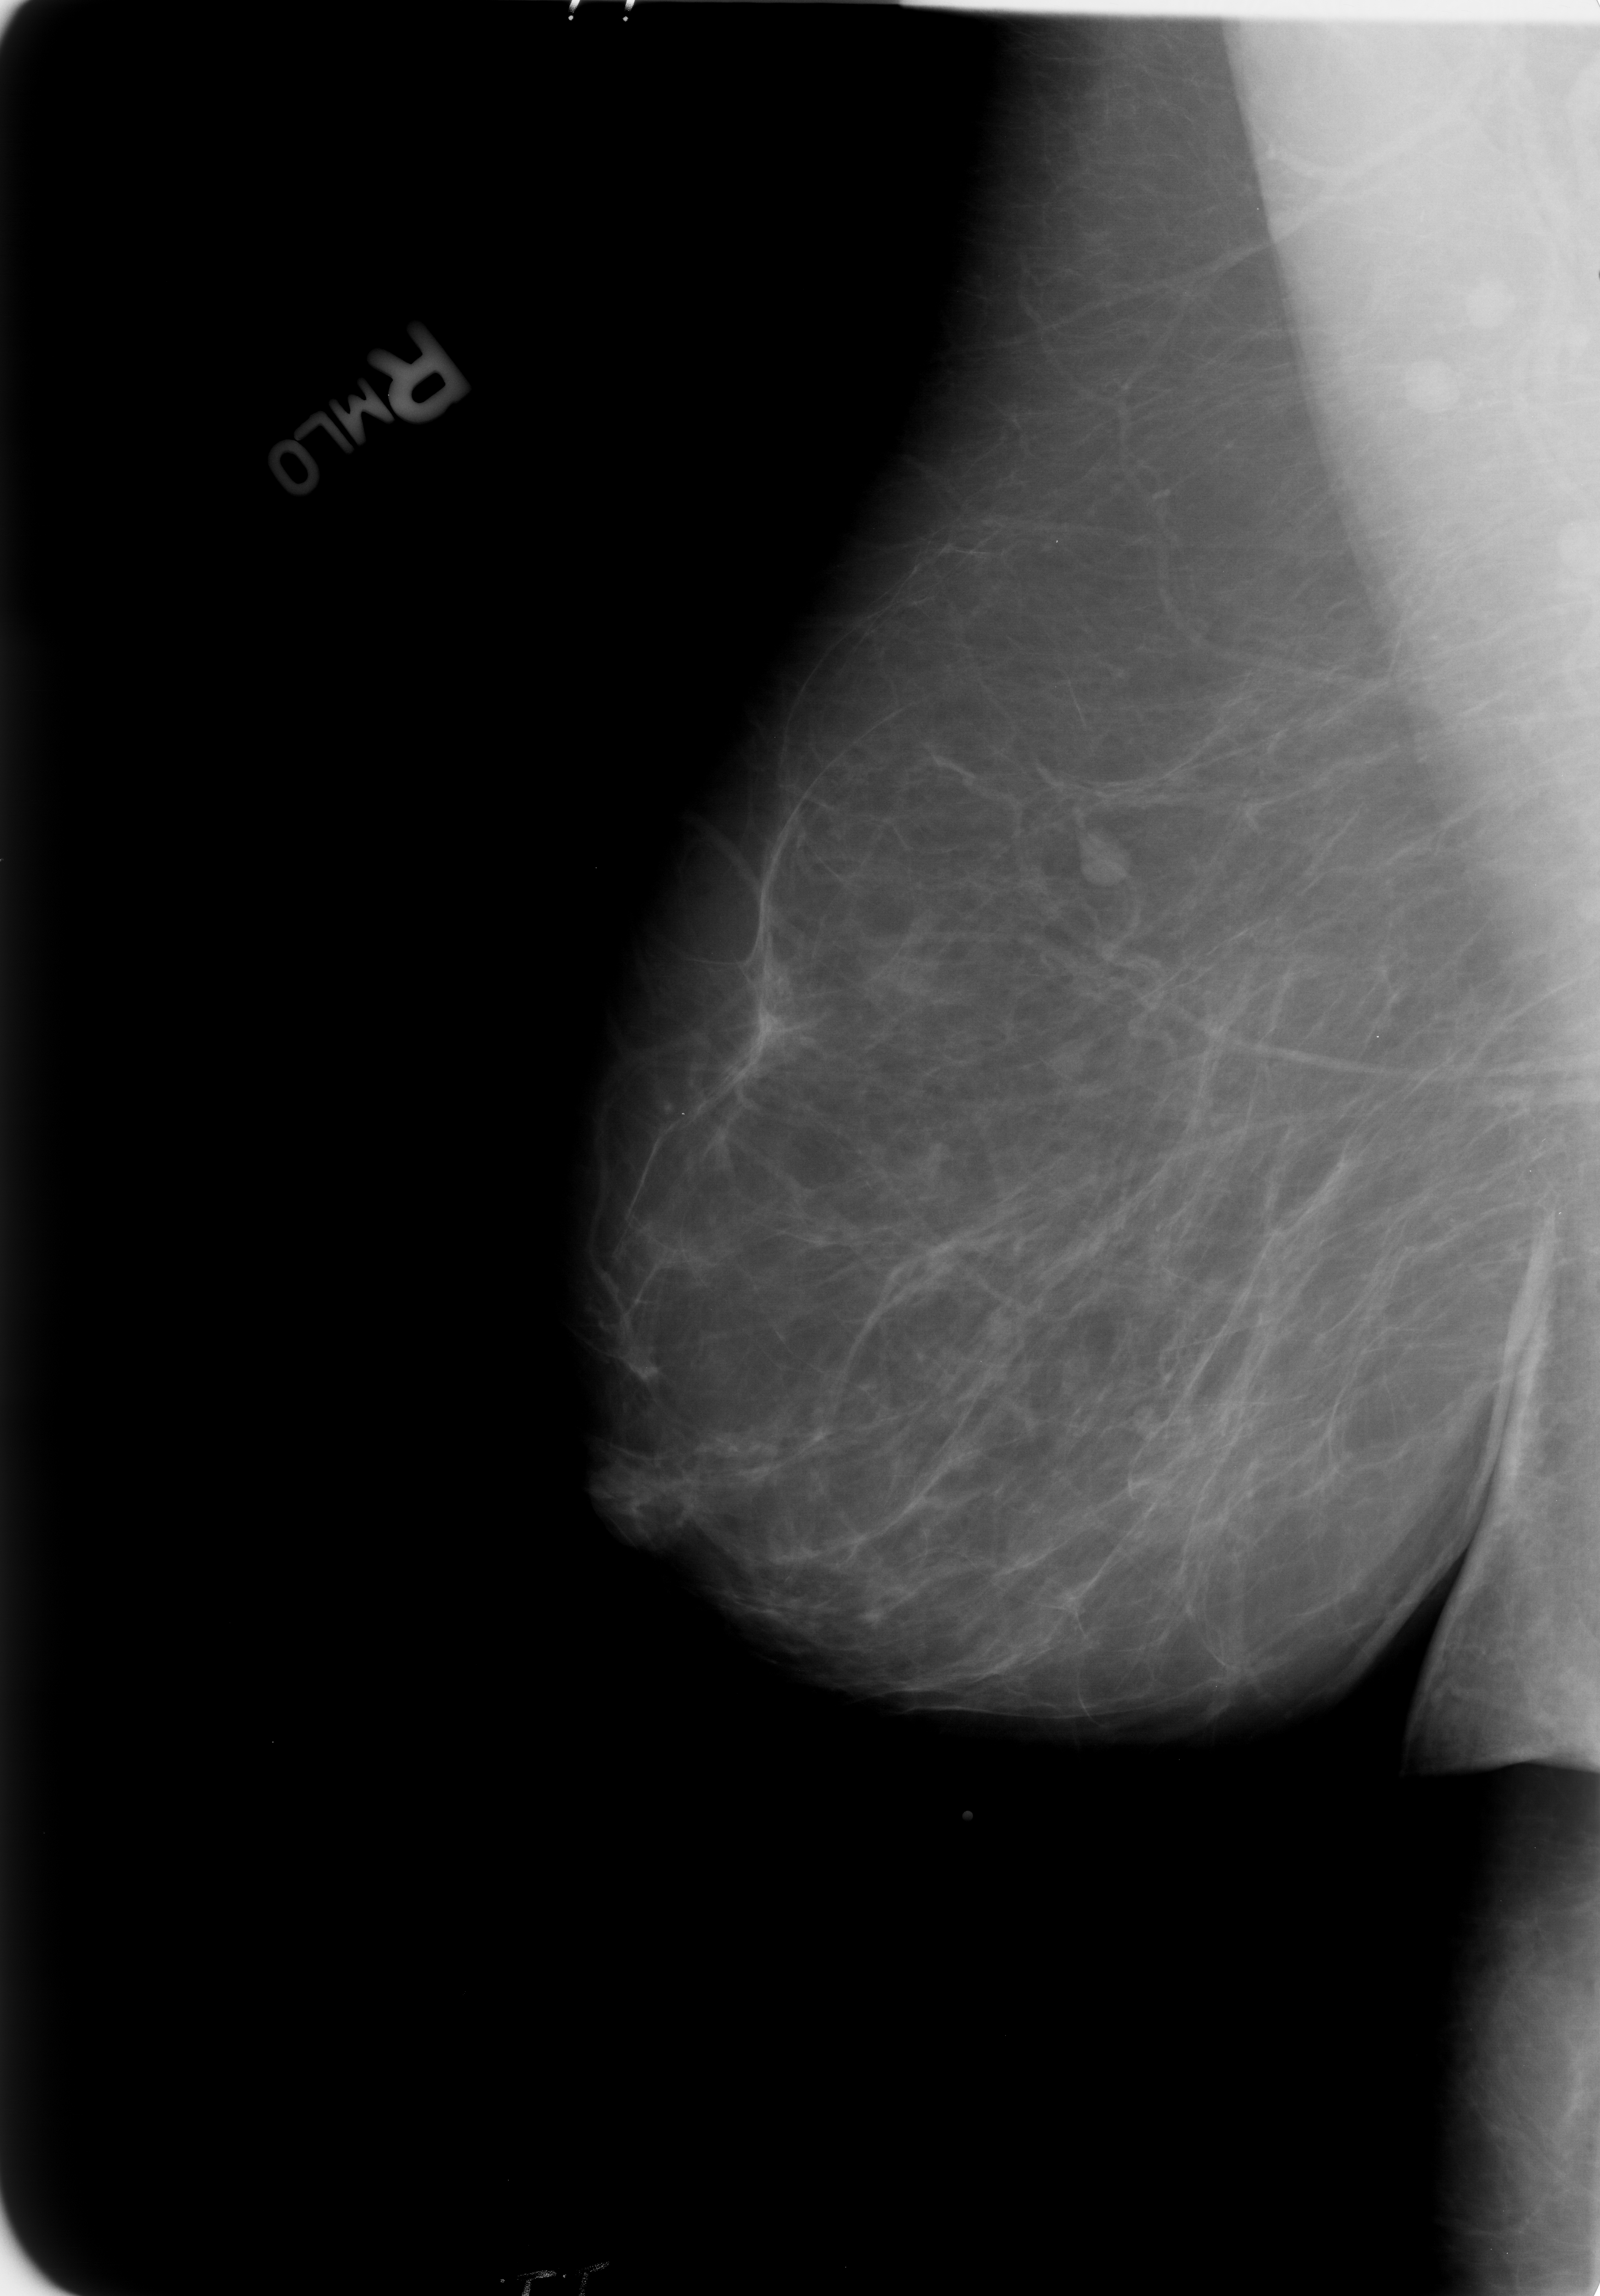
Mammogram (digitized film); right breast; MLO view; BI-RADS breast density category 1 (scale 1–4); 1600 × 2296 image matrix.
Expert-marked regions of interest on this film, with their recorded descriptors:
- mass, shape lymph node; BI-RADS assessment category 2; subtlety rating 3 on a 1 (subtle) to 5 (obvious) scale; outcome (as recorded, no biopsy): benign without callback (not worked up further): bounding box [x1, y1, x2, y2] px = [1061, 825, 1136, 894]